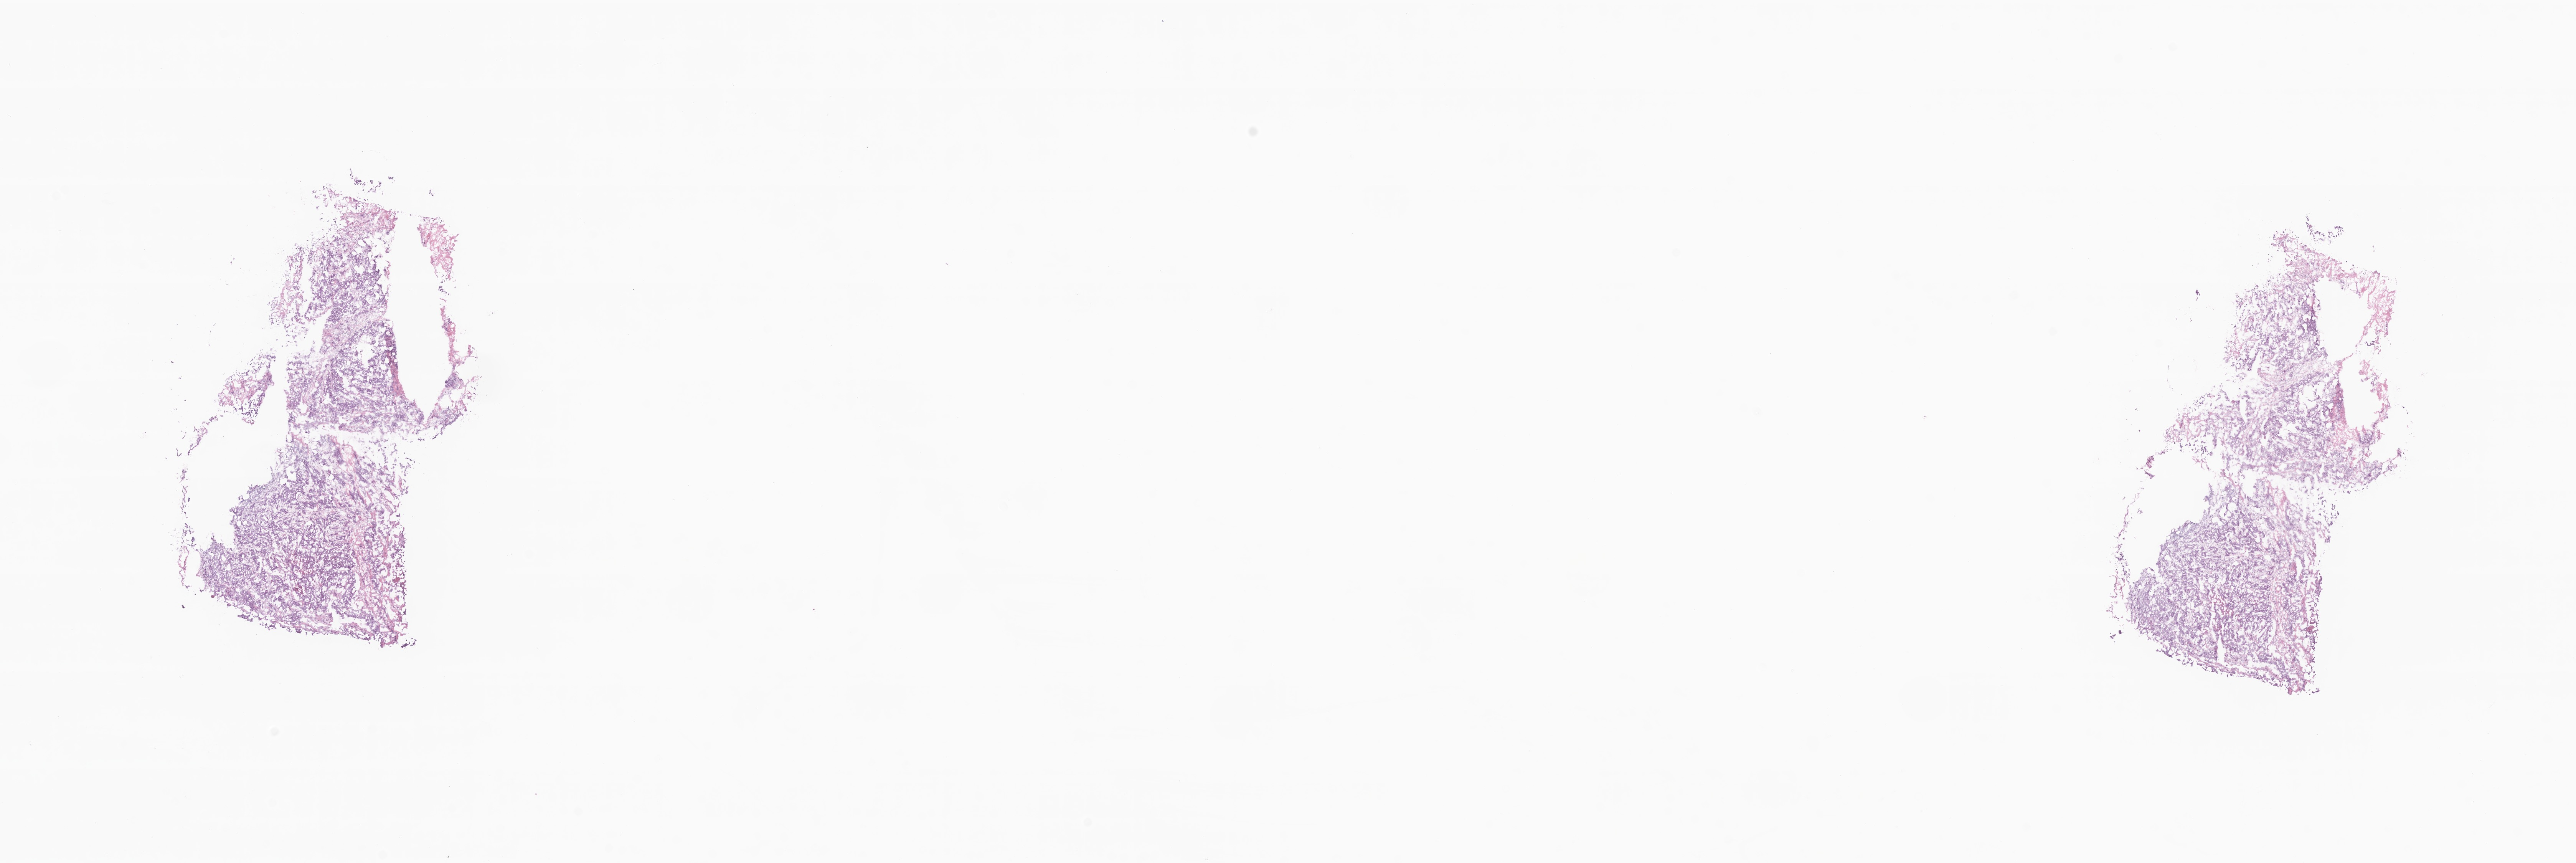
Haematoxylin and eosin whole-slide image — low-resolution overview of the scanned area, about 28.3 x 9.5 mm. Frozen section. Specimen: primary tumor. Anatomic site: breast (left). Patient: female, age at initial diagnosis 73 years. Composition of this section per pathologist review: tumor cells 64%, tumor nuclei 73%, stromal cells 11%, necrosis 2%, normal cells 23%. Infiltration values recorded for this section: lymphocyte infiltration 2%, monocyte infiltration 0%, neutrophil infiltration 0%.
* histologic diagnosis: Infiltrating duct carcinoma, NOS
* section: bottom of the tissue portion